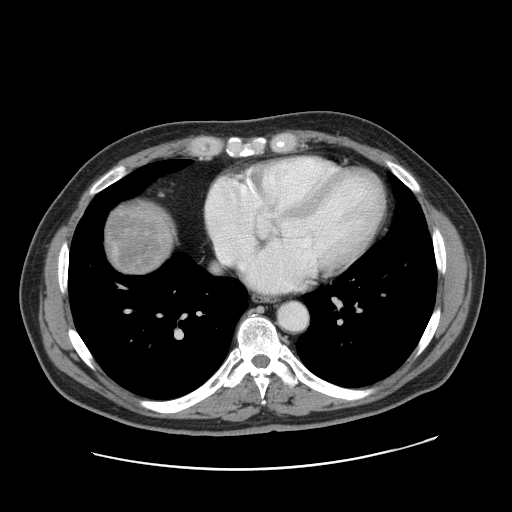
Contrast-enhanced abdominal CT, one axial slice; position 163 of 178 along the scan axis; 120 kVp; intravenous contrast given; soft-tissue window (W 400 / L 40 HU); 512 × 512 image matrix. Male patient, age 63 years. From the clinical record (not read from this slice): diagnosis: colorectal cancer liver metastases, imaged before liver resection; multiple liver metastases: yes; largest metastasis: 8 cm; chemotherapy before resection: no.
Annotated regions visible in this slice (manually delineated by an expert):
- liver: bounding box (x1, y1, x2, y2) in pixels: (104, 204, 173, 274)
- liver metastasis: (108, 208, 164, 273)